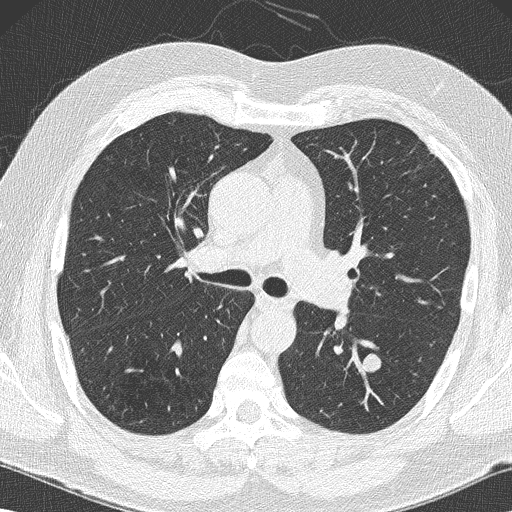
Low-dose screening chest CT, axial slice; first (baseline) screen; lung window (W 1500 / L -600 HU); 512 × 512 image matrix, field of view 350 × 350 mm. Male, age 59 years at enrolment.
- Expert reader's lesion annotation, bounding box <346,346,389,383> (left, top, right, bottom; pixels).
- The screening reader recorded 2 non-calcified nodules or masses ≥4 mm on this exam (left lower lobe, left lower lobe); which of them this box marks is not recorded.
- Official screen result: positive, change unspecified: nodule(s) >= 4 mm or enlarging nodule(s), mass(es), or other non-specific abnormalities suspicious for lung cancer.
- Participant outcome: lung cancer diagnosed 61 days after this screen — large cell carcinoma, NOS, left lower lobe, poorly differentiated (G3), stage IA (AJCC 6th edition), 14 mm at pathology.